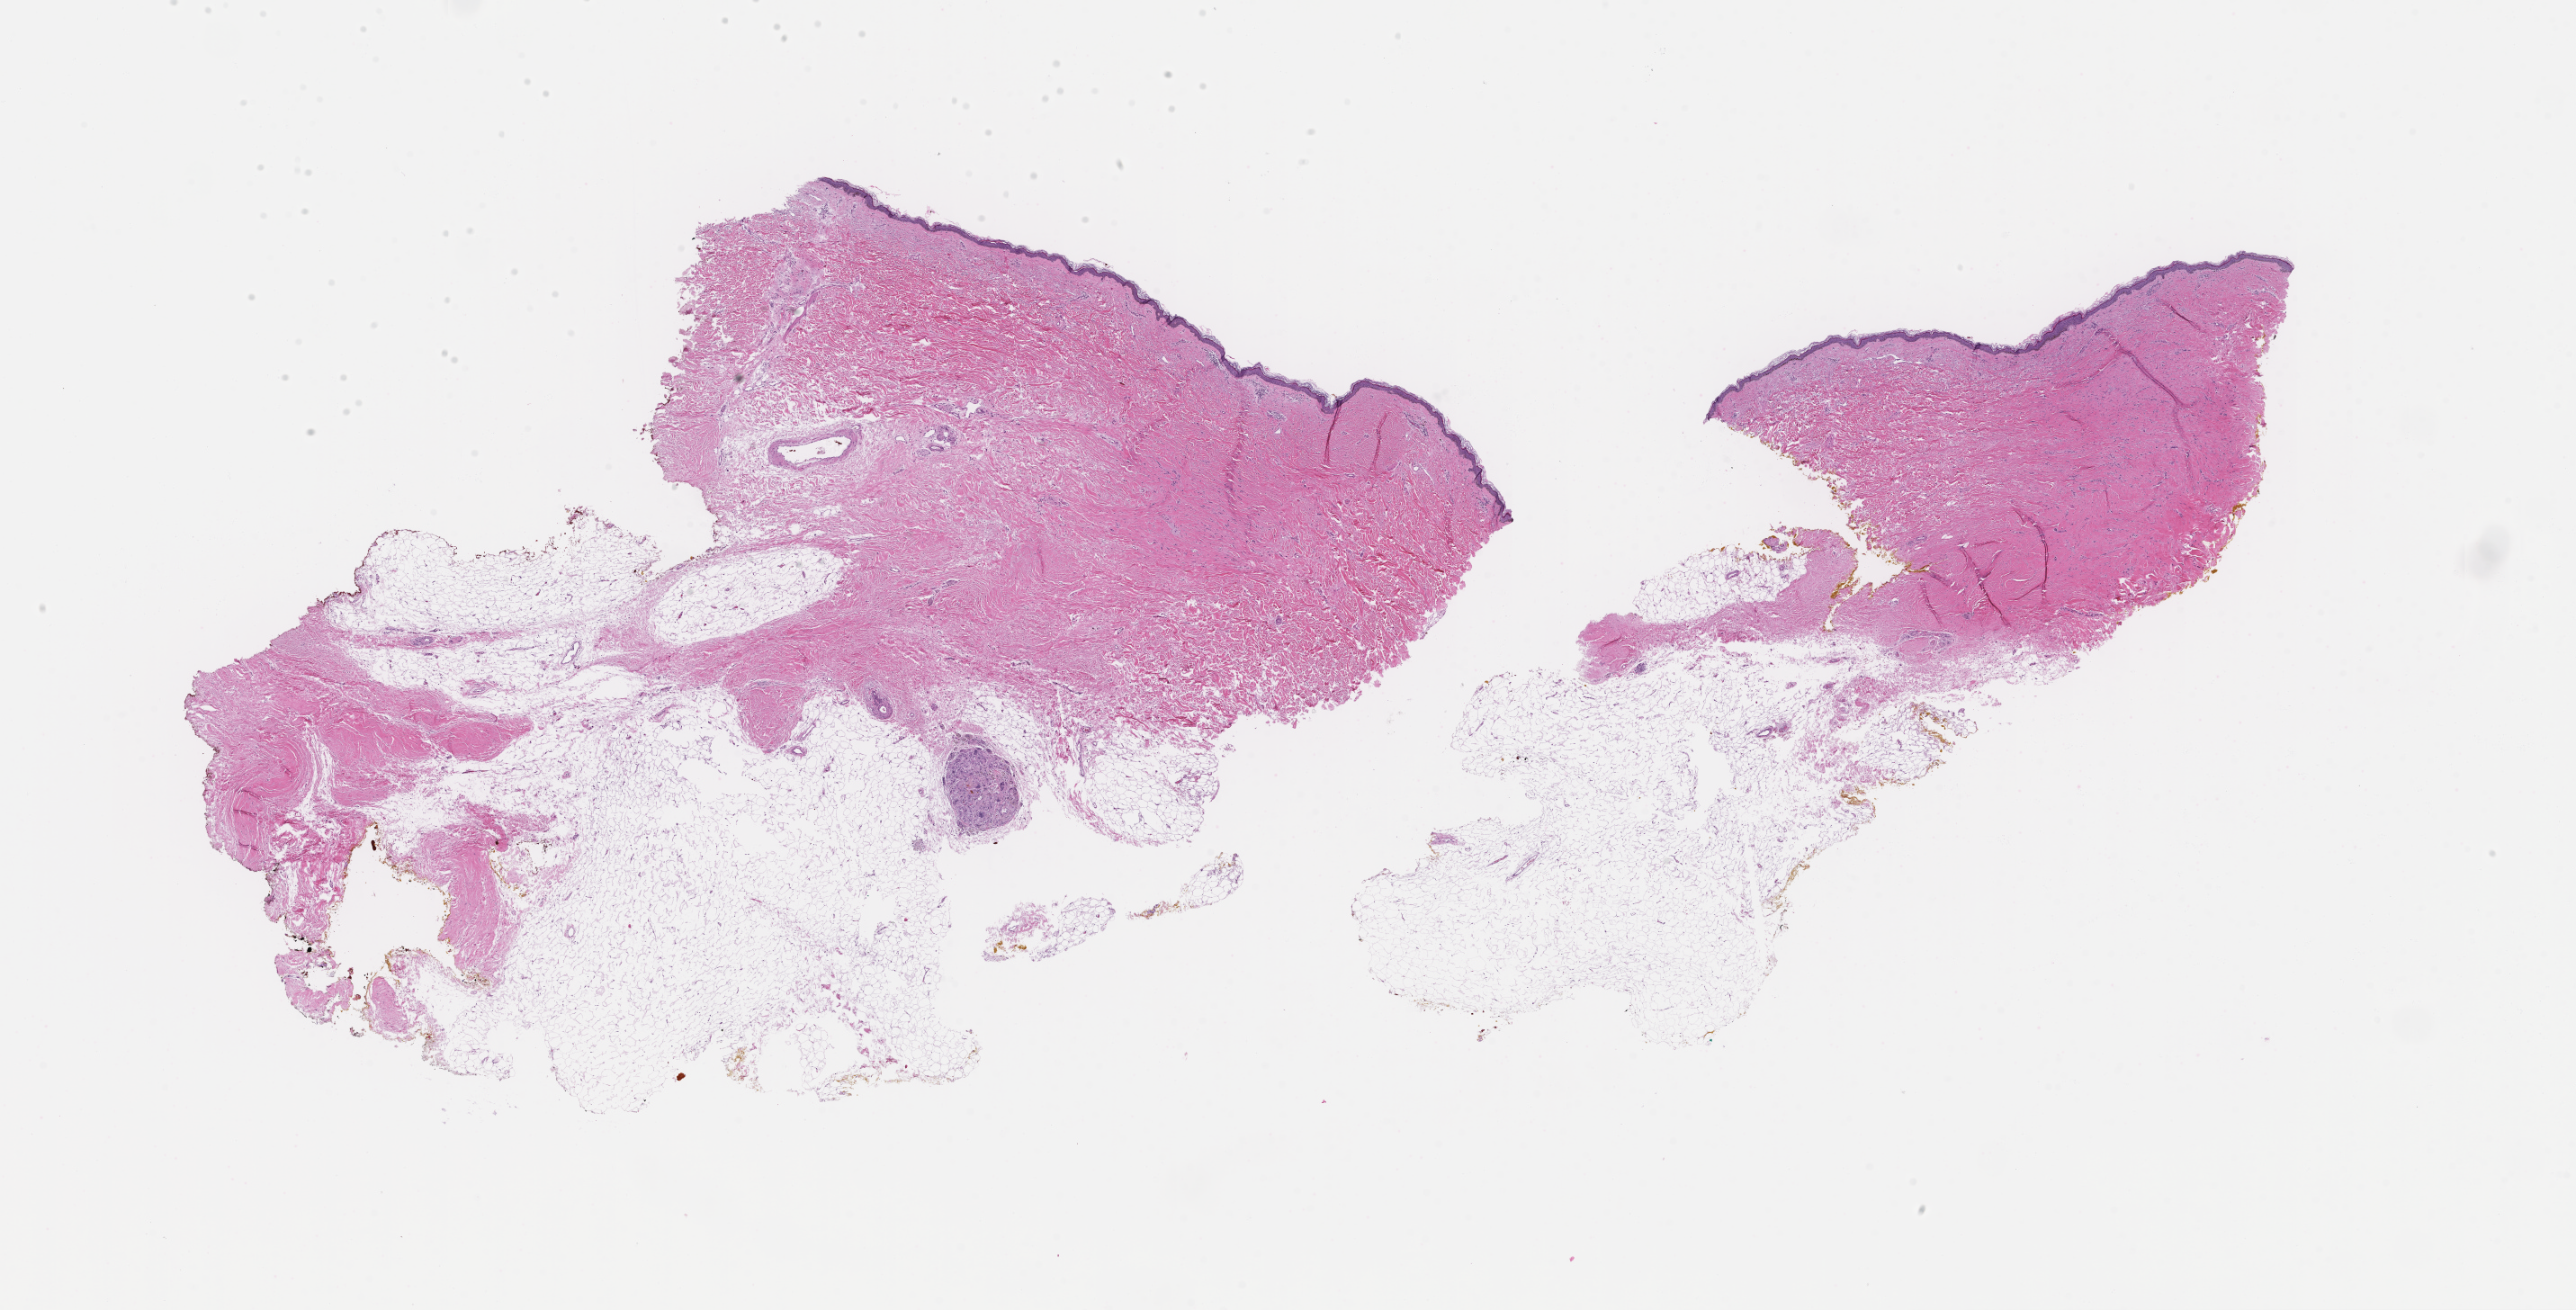
Haematoxylin and eosin whole-slide image — whole scanned area (about 23.1 x 11.8 mm) shown as a low-resolution overview; formalin-fixed paraffin-embedded section; archival tissue. Patient: female.
This section: metastatic tumor tissue. Primary diagnosis of the patient: Invasive Breast Carcinoma.